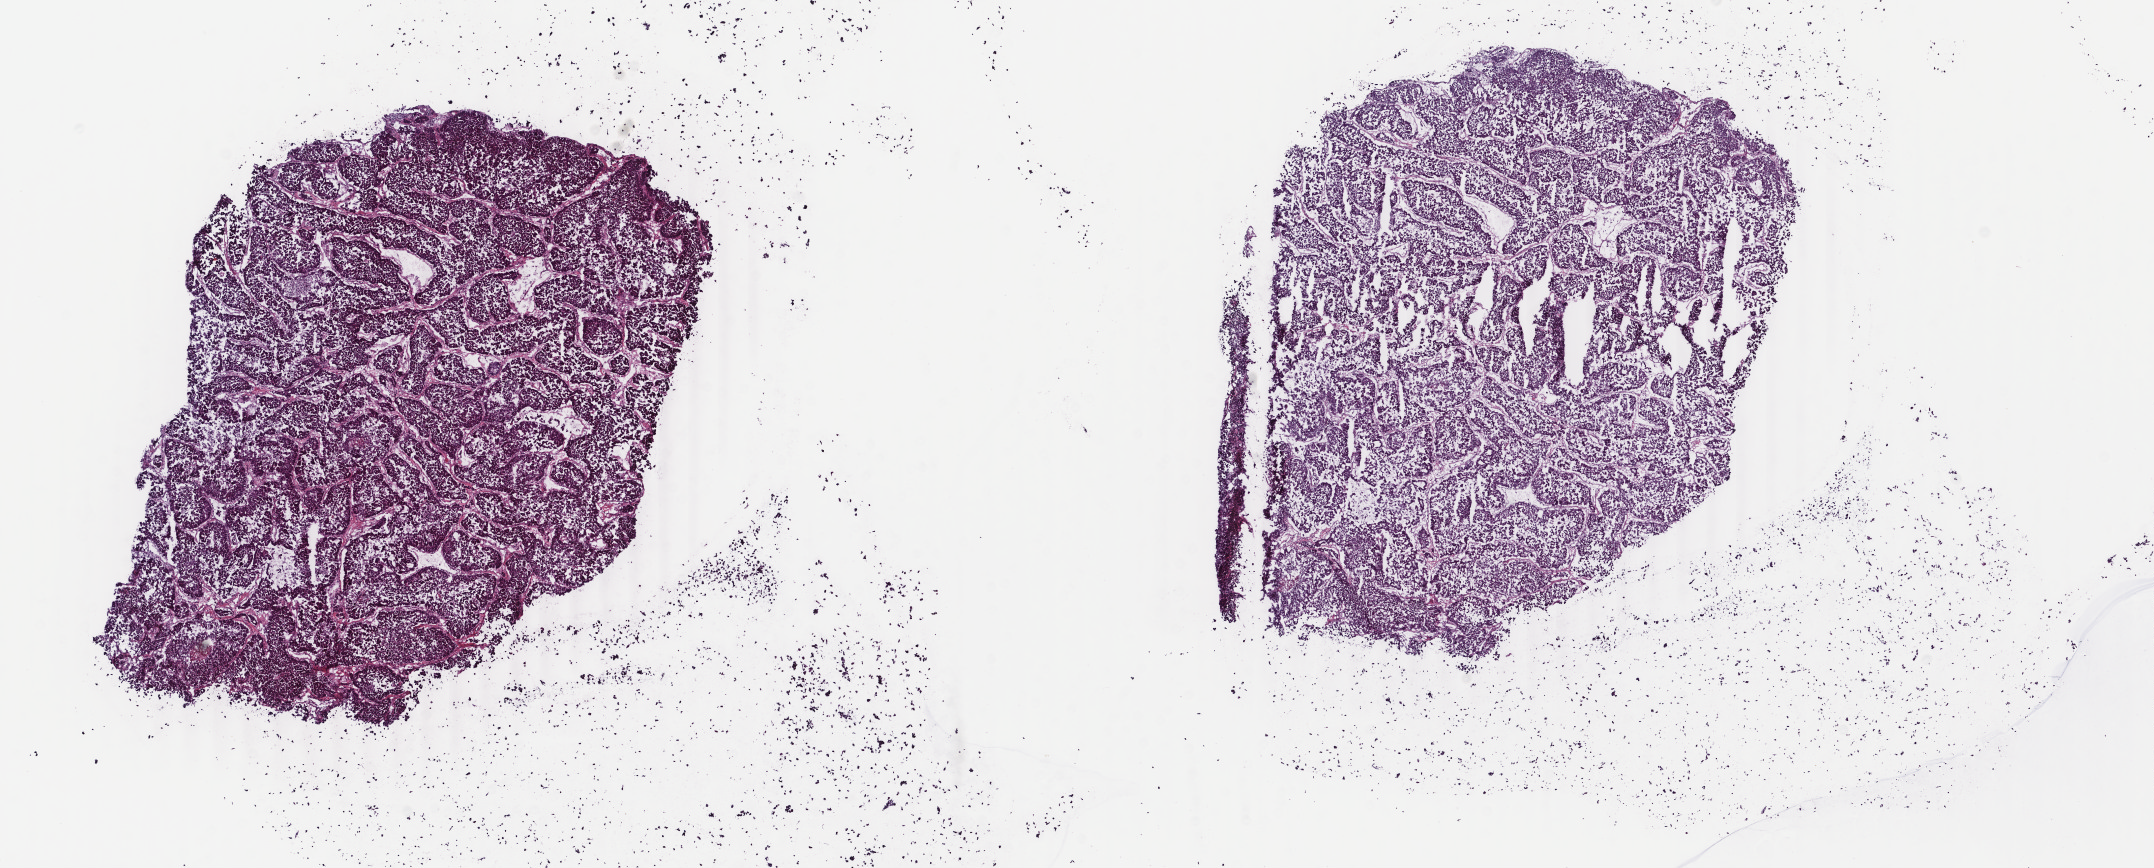
Whole-slide histology image, Hematoxylin and eosin (H&E) stained — low-resolution overview of the scanned area, about 17.1 x 6.9 mm. Frozen section from the top of the tissue portion. Sample: primary tumour, liver. Male patient; age at initial diagnosis 69 years. Histologic grade: G2 (moderately differentiated). Pathologist review of this section (percent, as recorded): tumour cells 95%, tumour nuclei 95%, normal cells 0%, stromal cells 0%, necrosis 5%. Inflammatory infiltration, as recorded: lymphocyte infiltration 0%, monocyte infiltration 0%, neutrophil infiltration 0%.
Histologic diagnosis: Hepatocellular carcinoma, NOS.